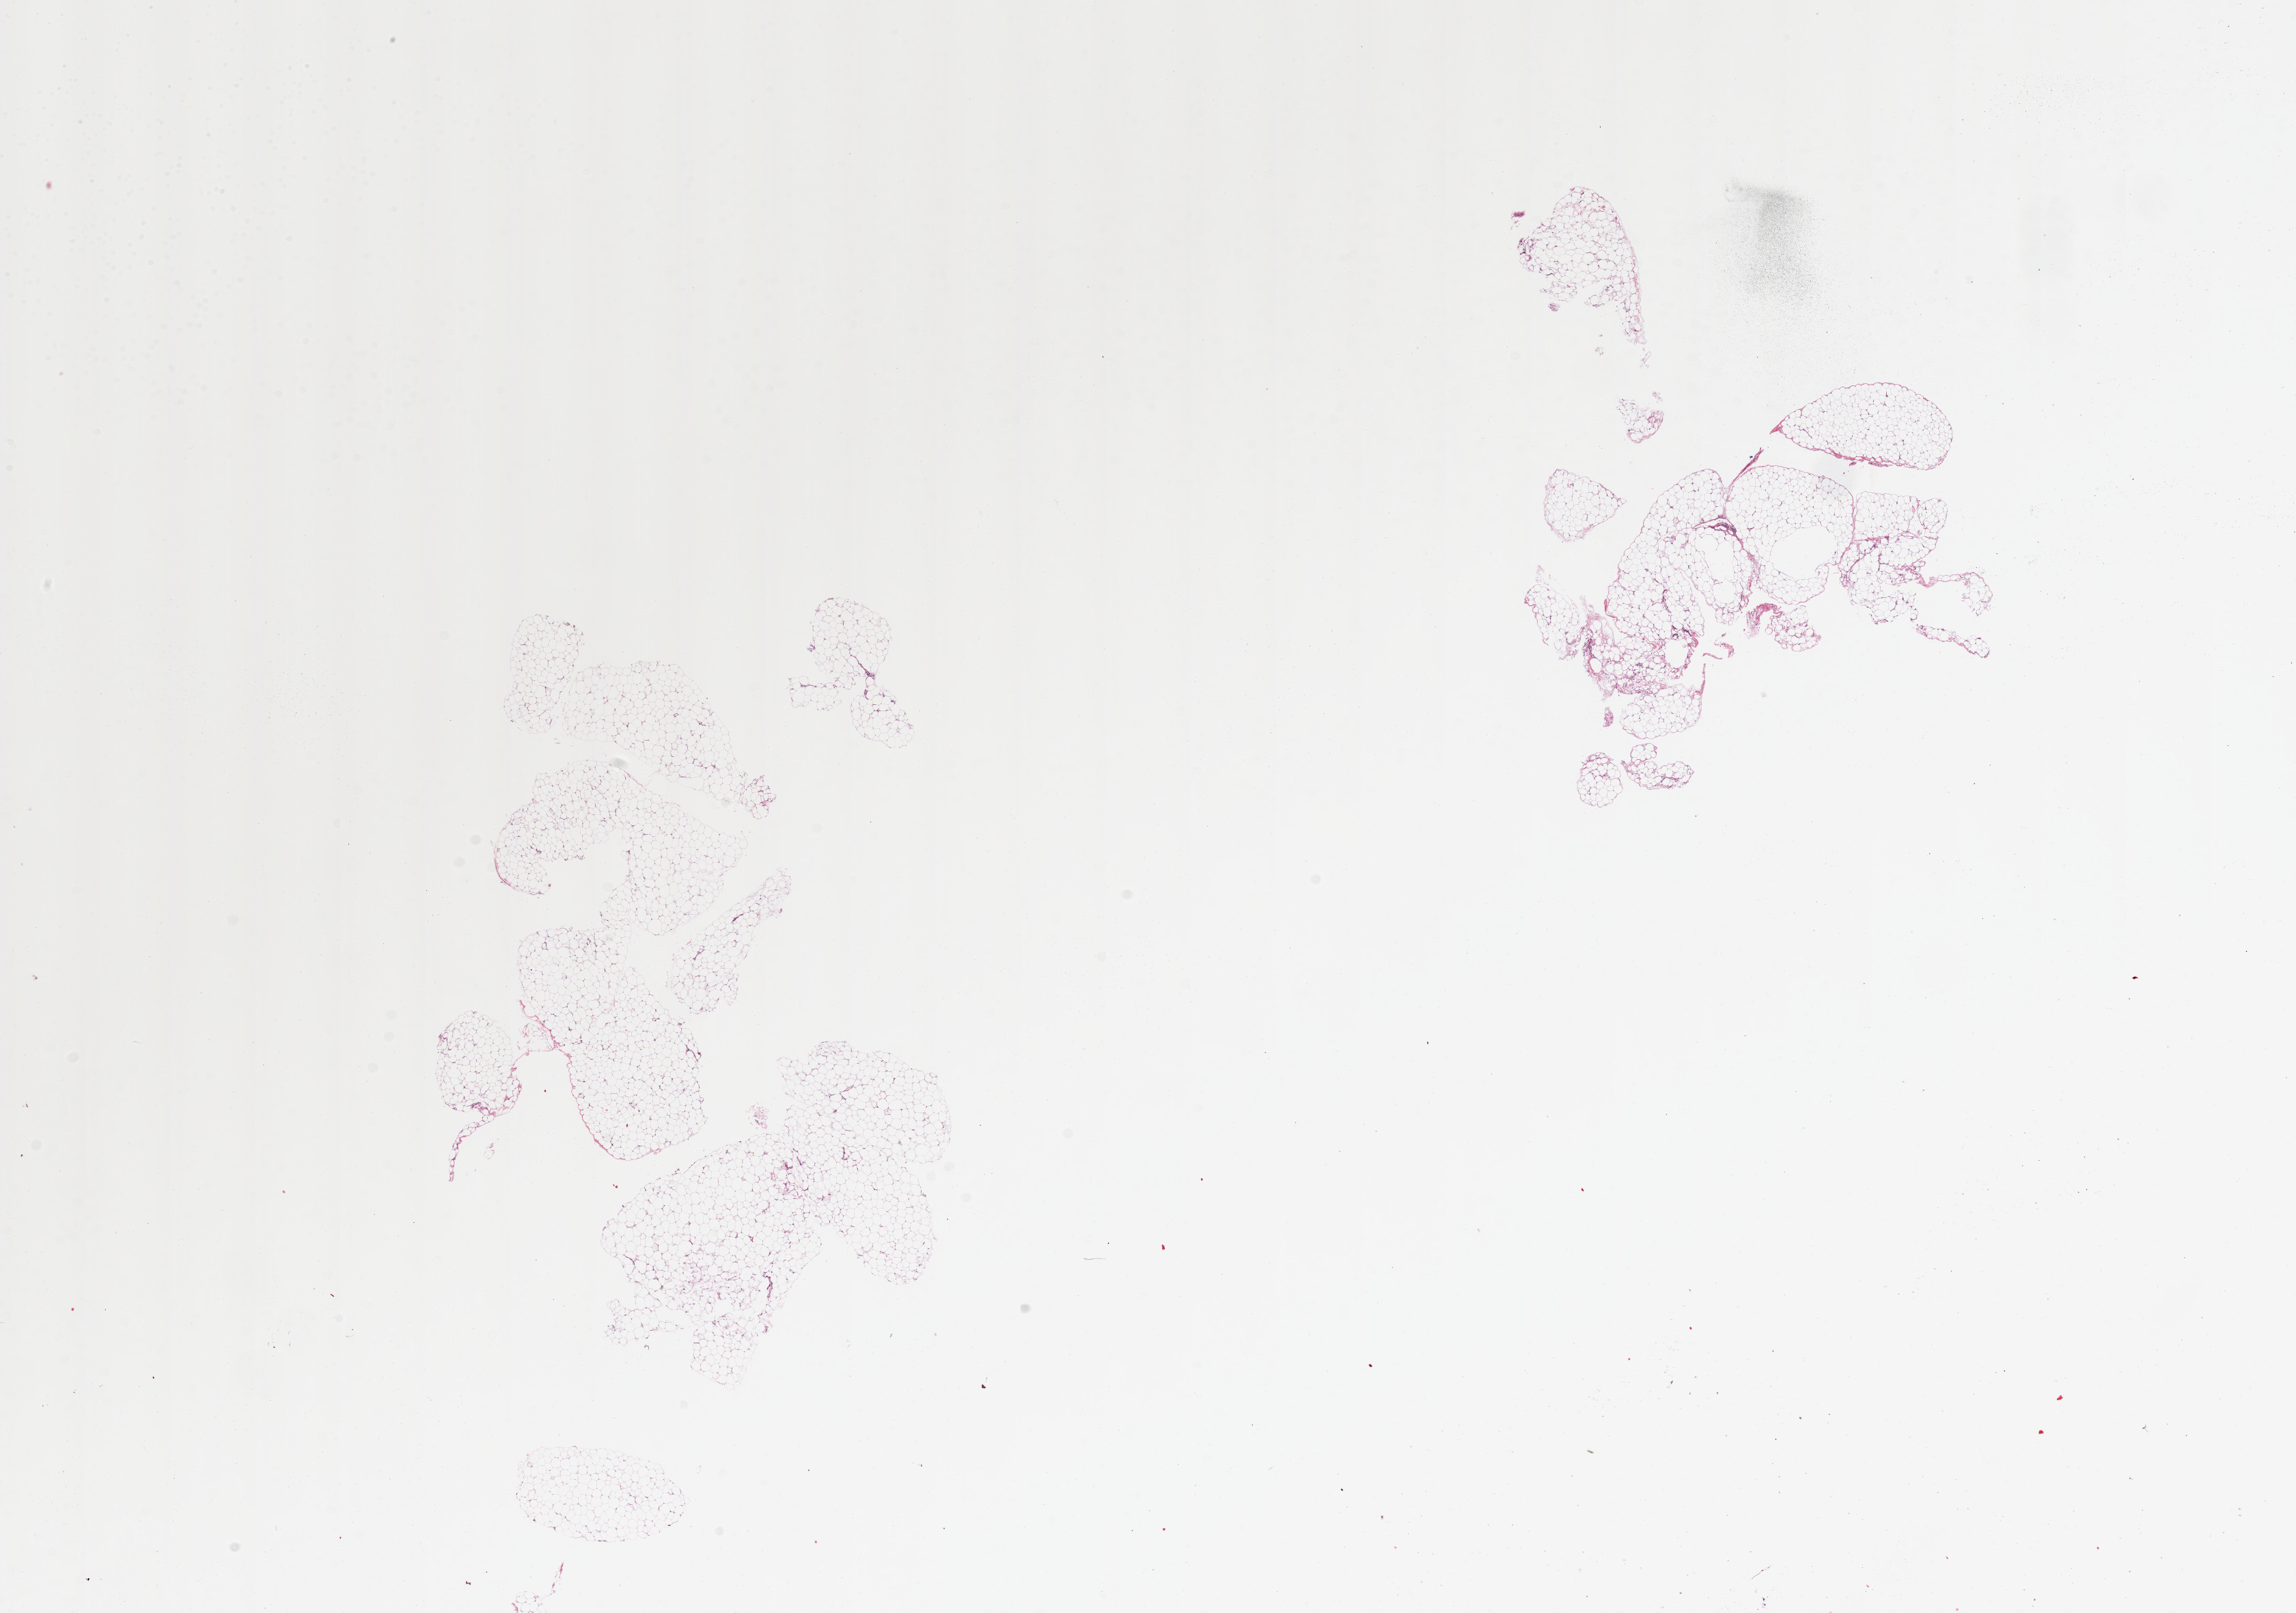
Whole-slide image, hematoxylin and eosin (H&E) stain, brightfield — whole scanned area (about 26.6 x 18.7 mm, from a 20x scan) shown as a low-resolution overview. PAXgene-fixed, paraffin-embedded tissue. Sampled site (target tissue): omentum. Tissue donor sample. Donor sex: male.
Pathologist's review note for this sample: 2 pieces.